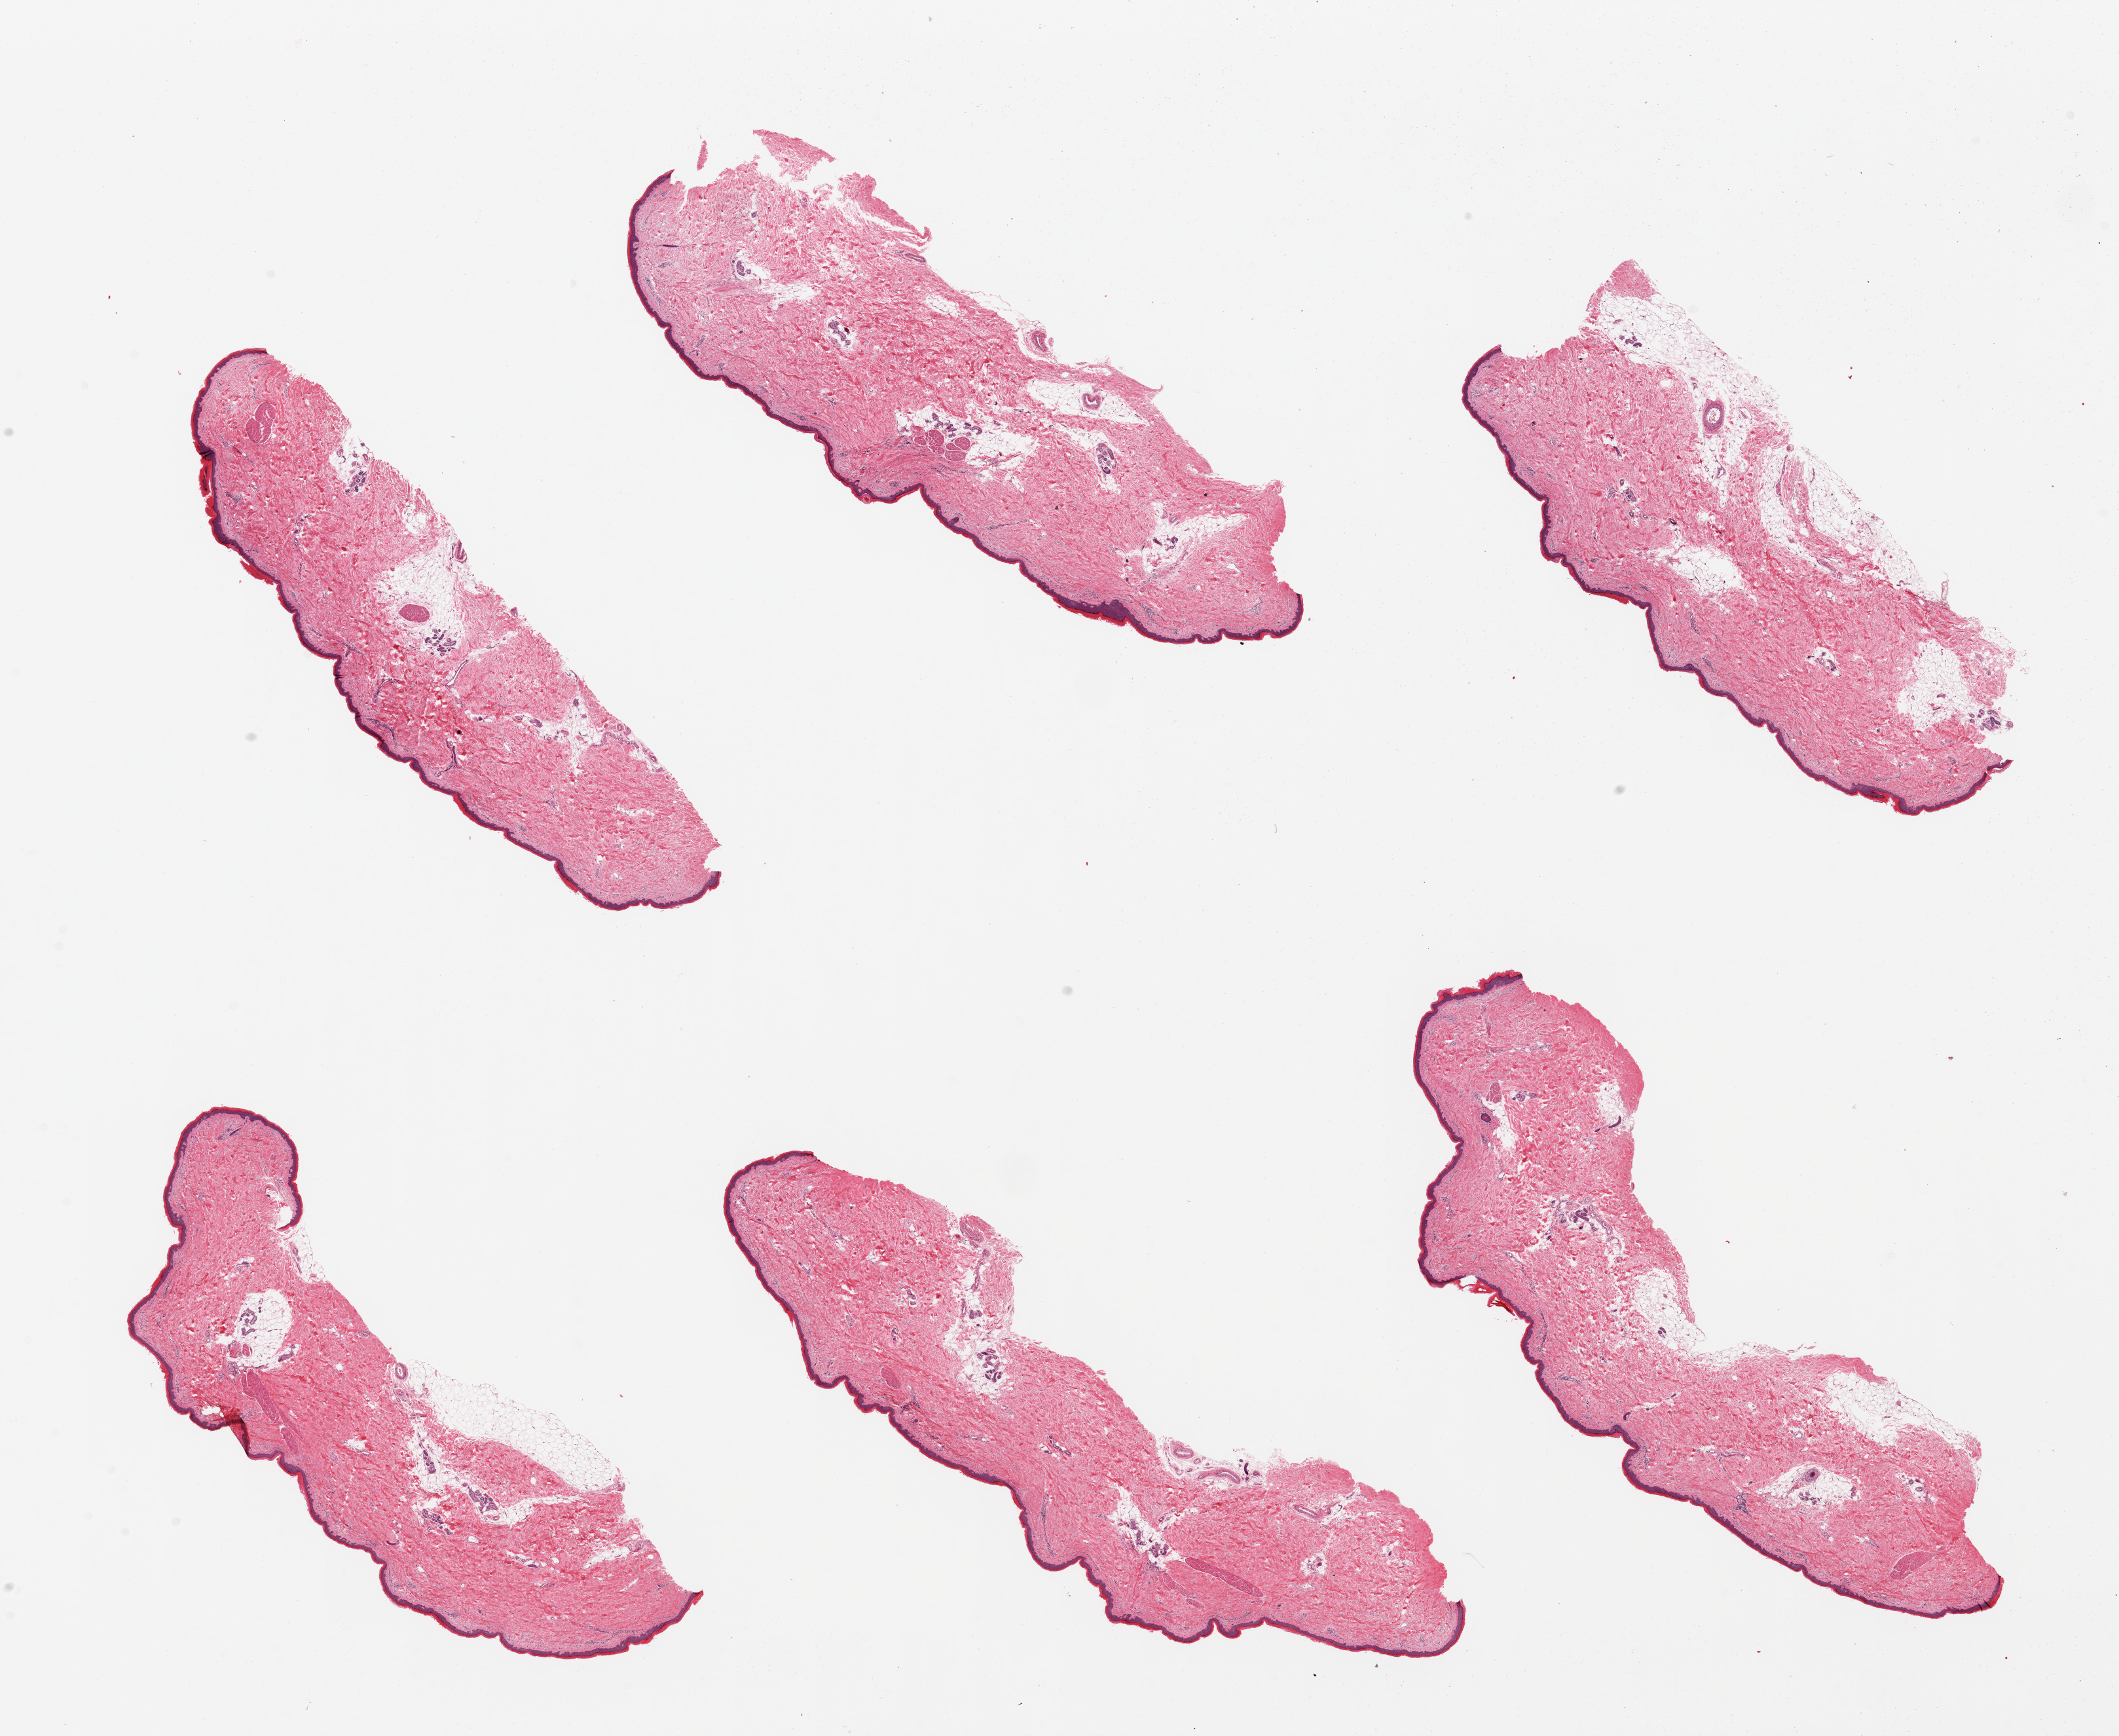
Digitized H&E-stained section — whole scanned area (about 25.6 x 21.0 mm, from a 20x scan) shown as a low-resolution overview; PAXgene-fixed, paraffin-embedded tissue; section of skin of lower leg (target tissue); tissue donor sample. Donor sex: female.
Reviewer comment on this tissue sample: 6 pieces, trace fat (~0.5mm) on a few sections. Squamous epithelium is ~50-60 microns thick.